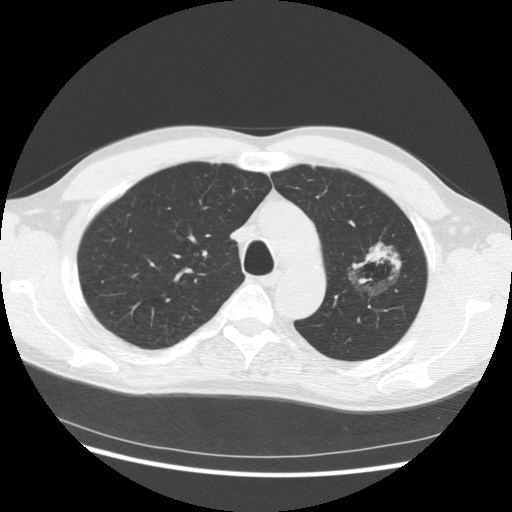
Low-dose screening chest CT, one axial slice; slice 105 of 145 in the series (ordered by position); reconstruction kernel STANDARD; 140 kVp; lung window (W 1500 / L -600 HU); 2.5 mm slice thickness; 512 × 512 image matrix.
Annotated regions visible in this slice (expert manual segmentation):
- lesion 1 (tumor, upper lobe of left lung): bounding box [x1, y1, x2, y2] px = [366, 244, 401, 269]